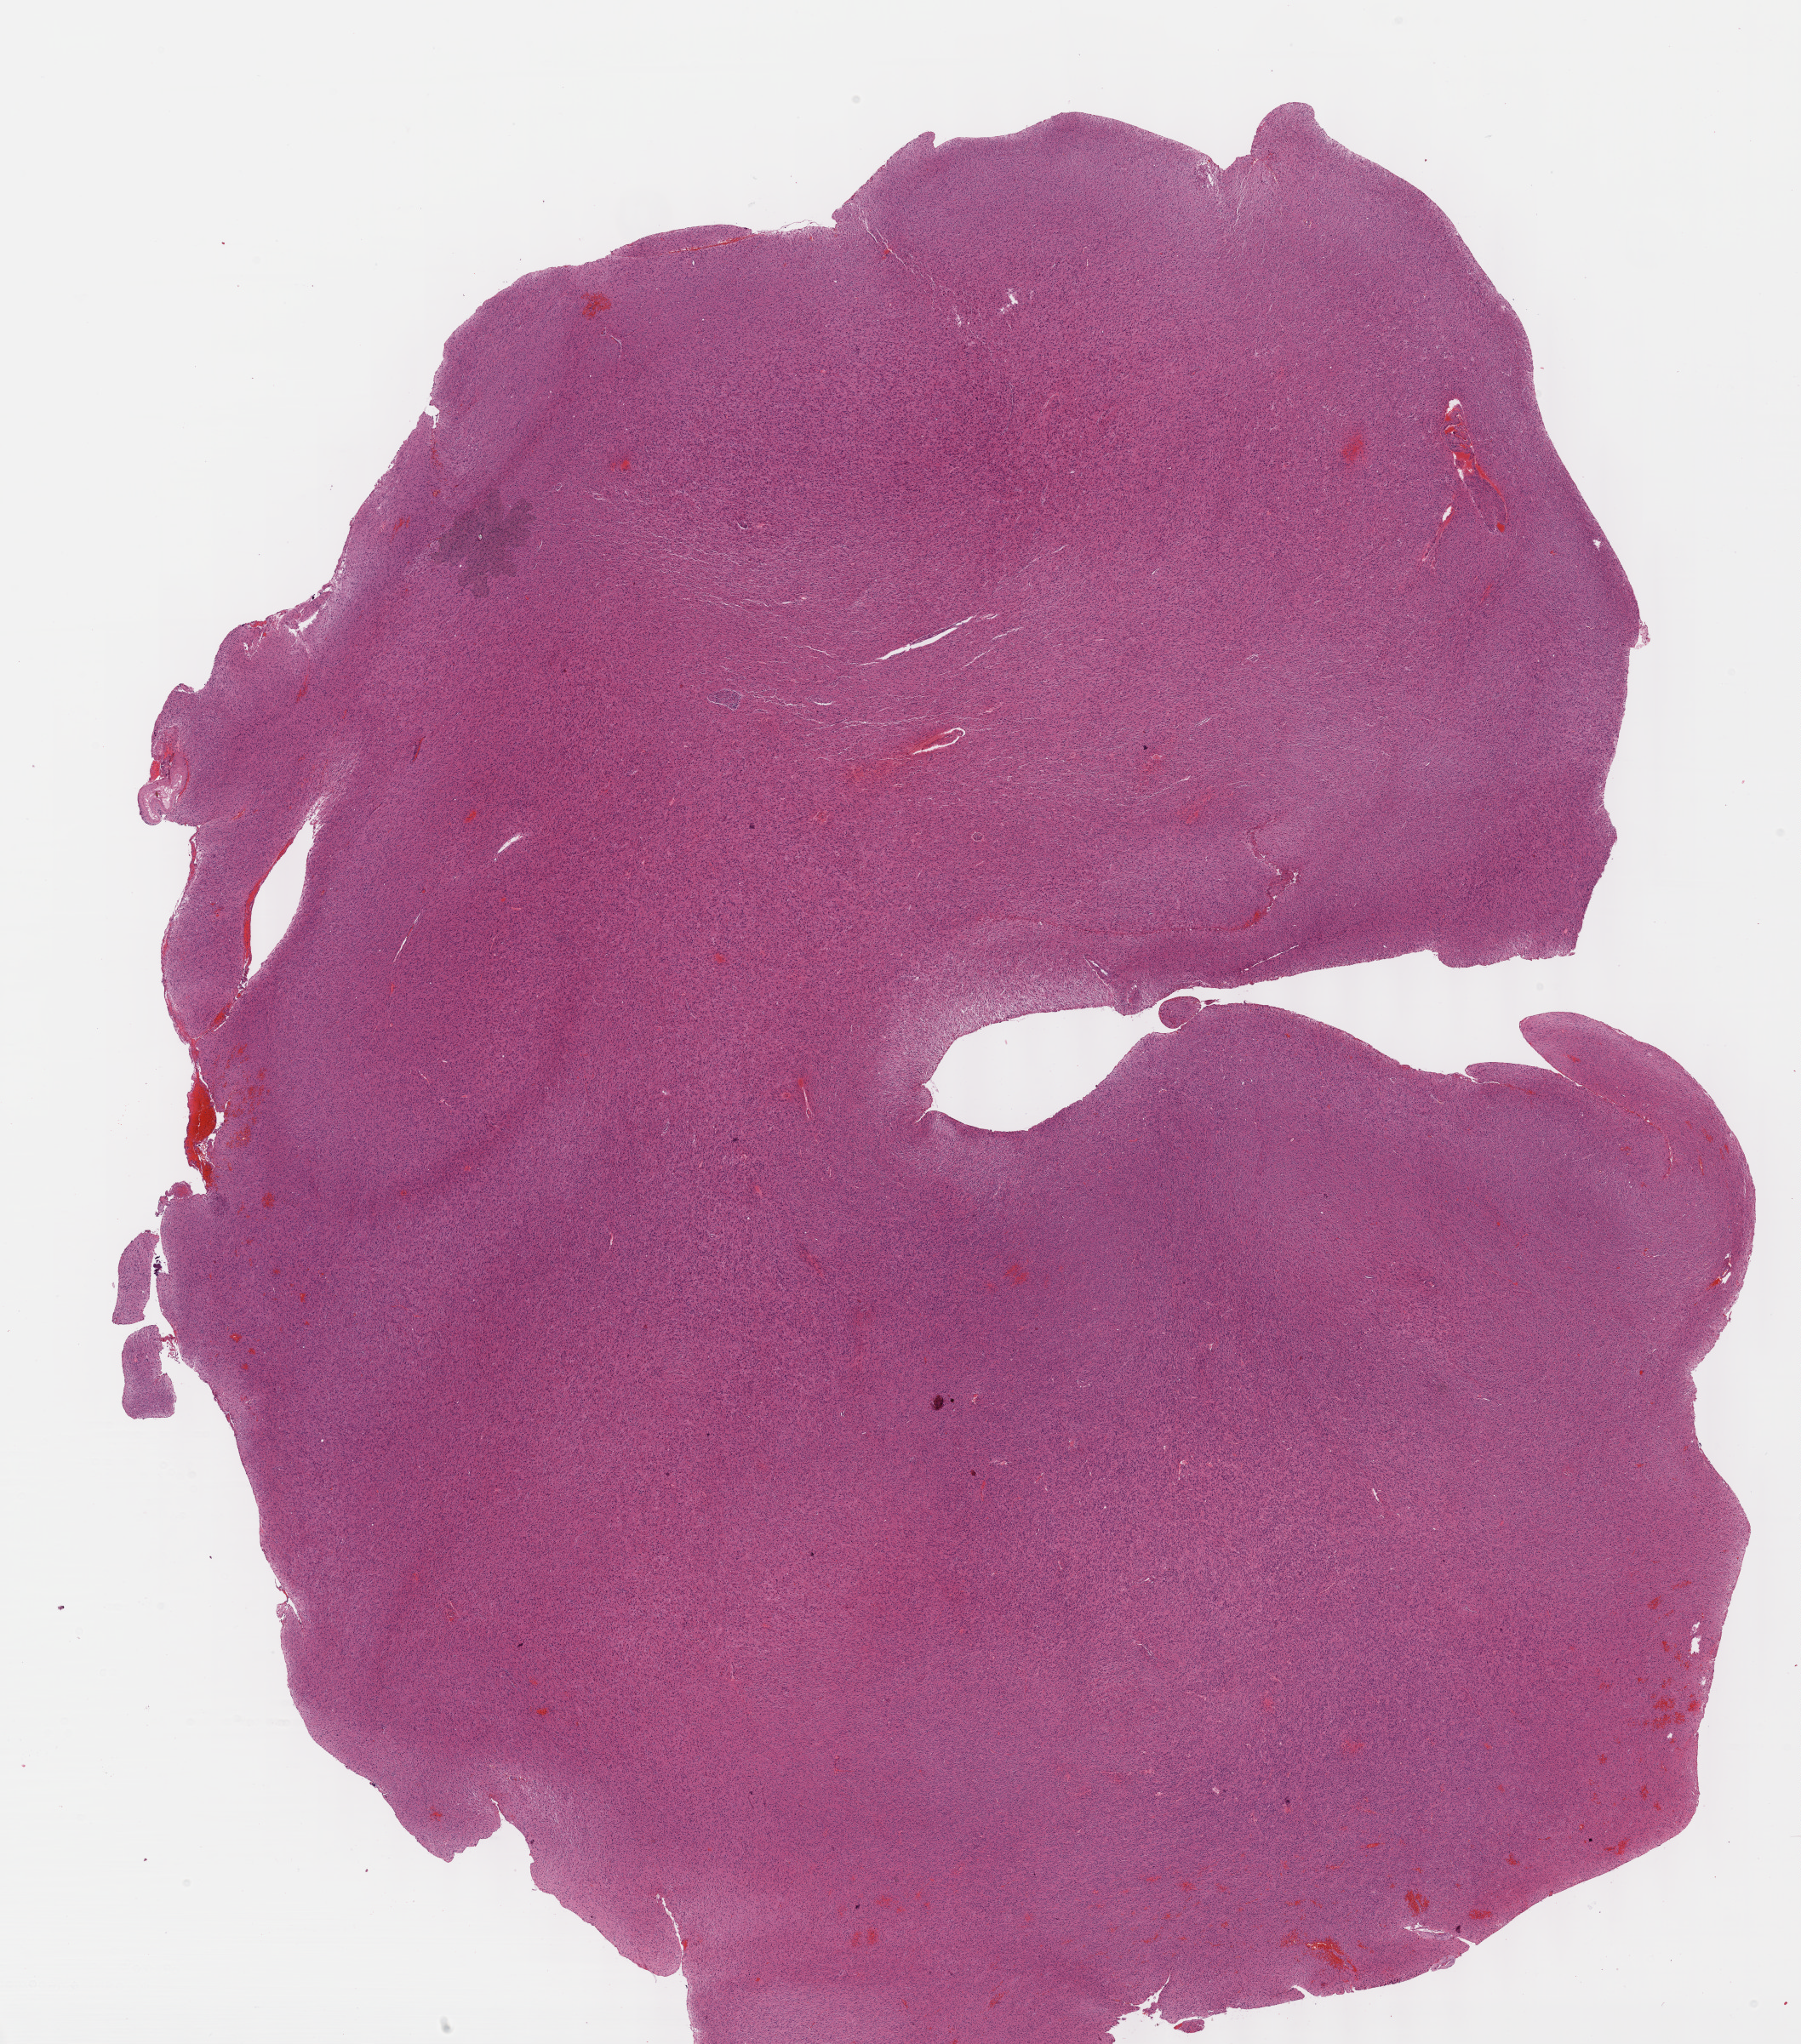
Whole-slide histology image, H&E-stained — whole scanned area (about 17.1 x 19.4 mm, acquisition: 40x scan) shown as a low-resolution overview, formalin-fixed paraffin-embedded (FFPE) diagnostic section, brain, primary tumour sample. Patient: female, age at initial diagnosis 70 years.
Pathologic diagnosis: Astrocytoma, anaplastic (cerebrum).